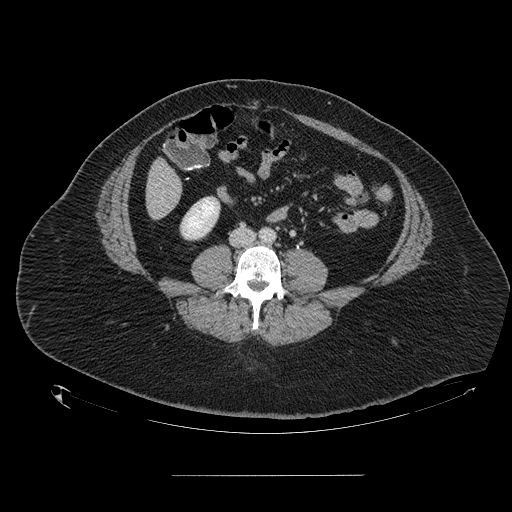
Contrast-enhanced abdominal CT, one axial slice. Position 19 of 164 along the scan axis. Intravenous contrast given. Soft-tissue window (W 400 / L 40 HU). 2.5 mm slice thickness. 512 × 512 image matrix. Female patient, age 52 years. From the clinical record (not read from this slice): diagnosis: colorectal cancer liver metastases, imaged before liver resection; multiple liver metastases: yes; largest metastasis: 3.5 cm.
Annotated regions visible in this slice (expert manual segmentation):
- liver: bounding box <147,161,181,218> (left, top, right, bottom; pixels)